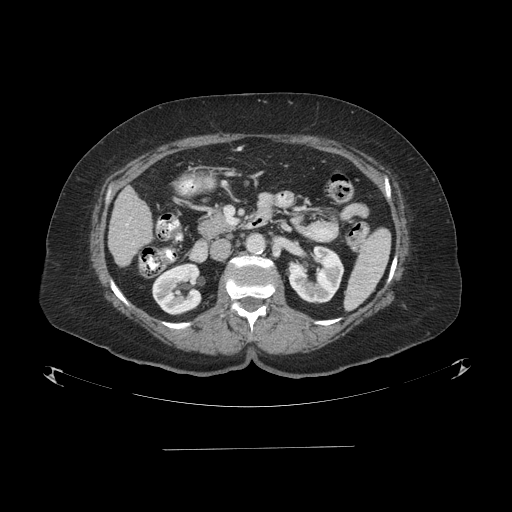
Contrast-enhanced abdominal CT (liver protocol), one axial slice; position 29 of 103 along the scan axis; reconstruction kernel STANDARD; one of 2 acquisitions stored at this slice position; soft-tissue window (W 400 / L 40 HU); 2.5 mm slice thickness; 512 × 512 image matrix. From the clinical record (not read from this slice): diagnosis: hepatocellular carcinoma (patient treated with transarterial chemoembolisation; whether this scan precedes or follows treatment is not stated here); TNM stage (as recorded): Stage-IIIA; Child-Pugh class: A; tumour differentiation: poorly differentiated; tumour nodularity: multinodular.
Annotated regions visible in this slice (semi-automatically segmented with operator editing):
- liver parenchyma outside the tumour (the mass and vessels are separate outlines, so this box may not span the whole liver): bounding box [x1, y1, x2, y2] px = [108, 186, 152, 266]